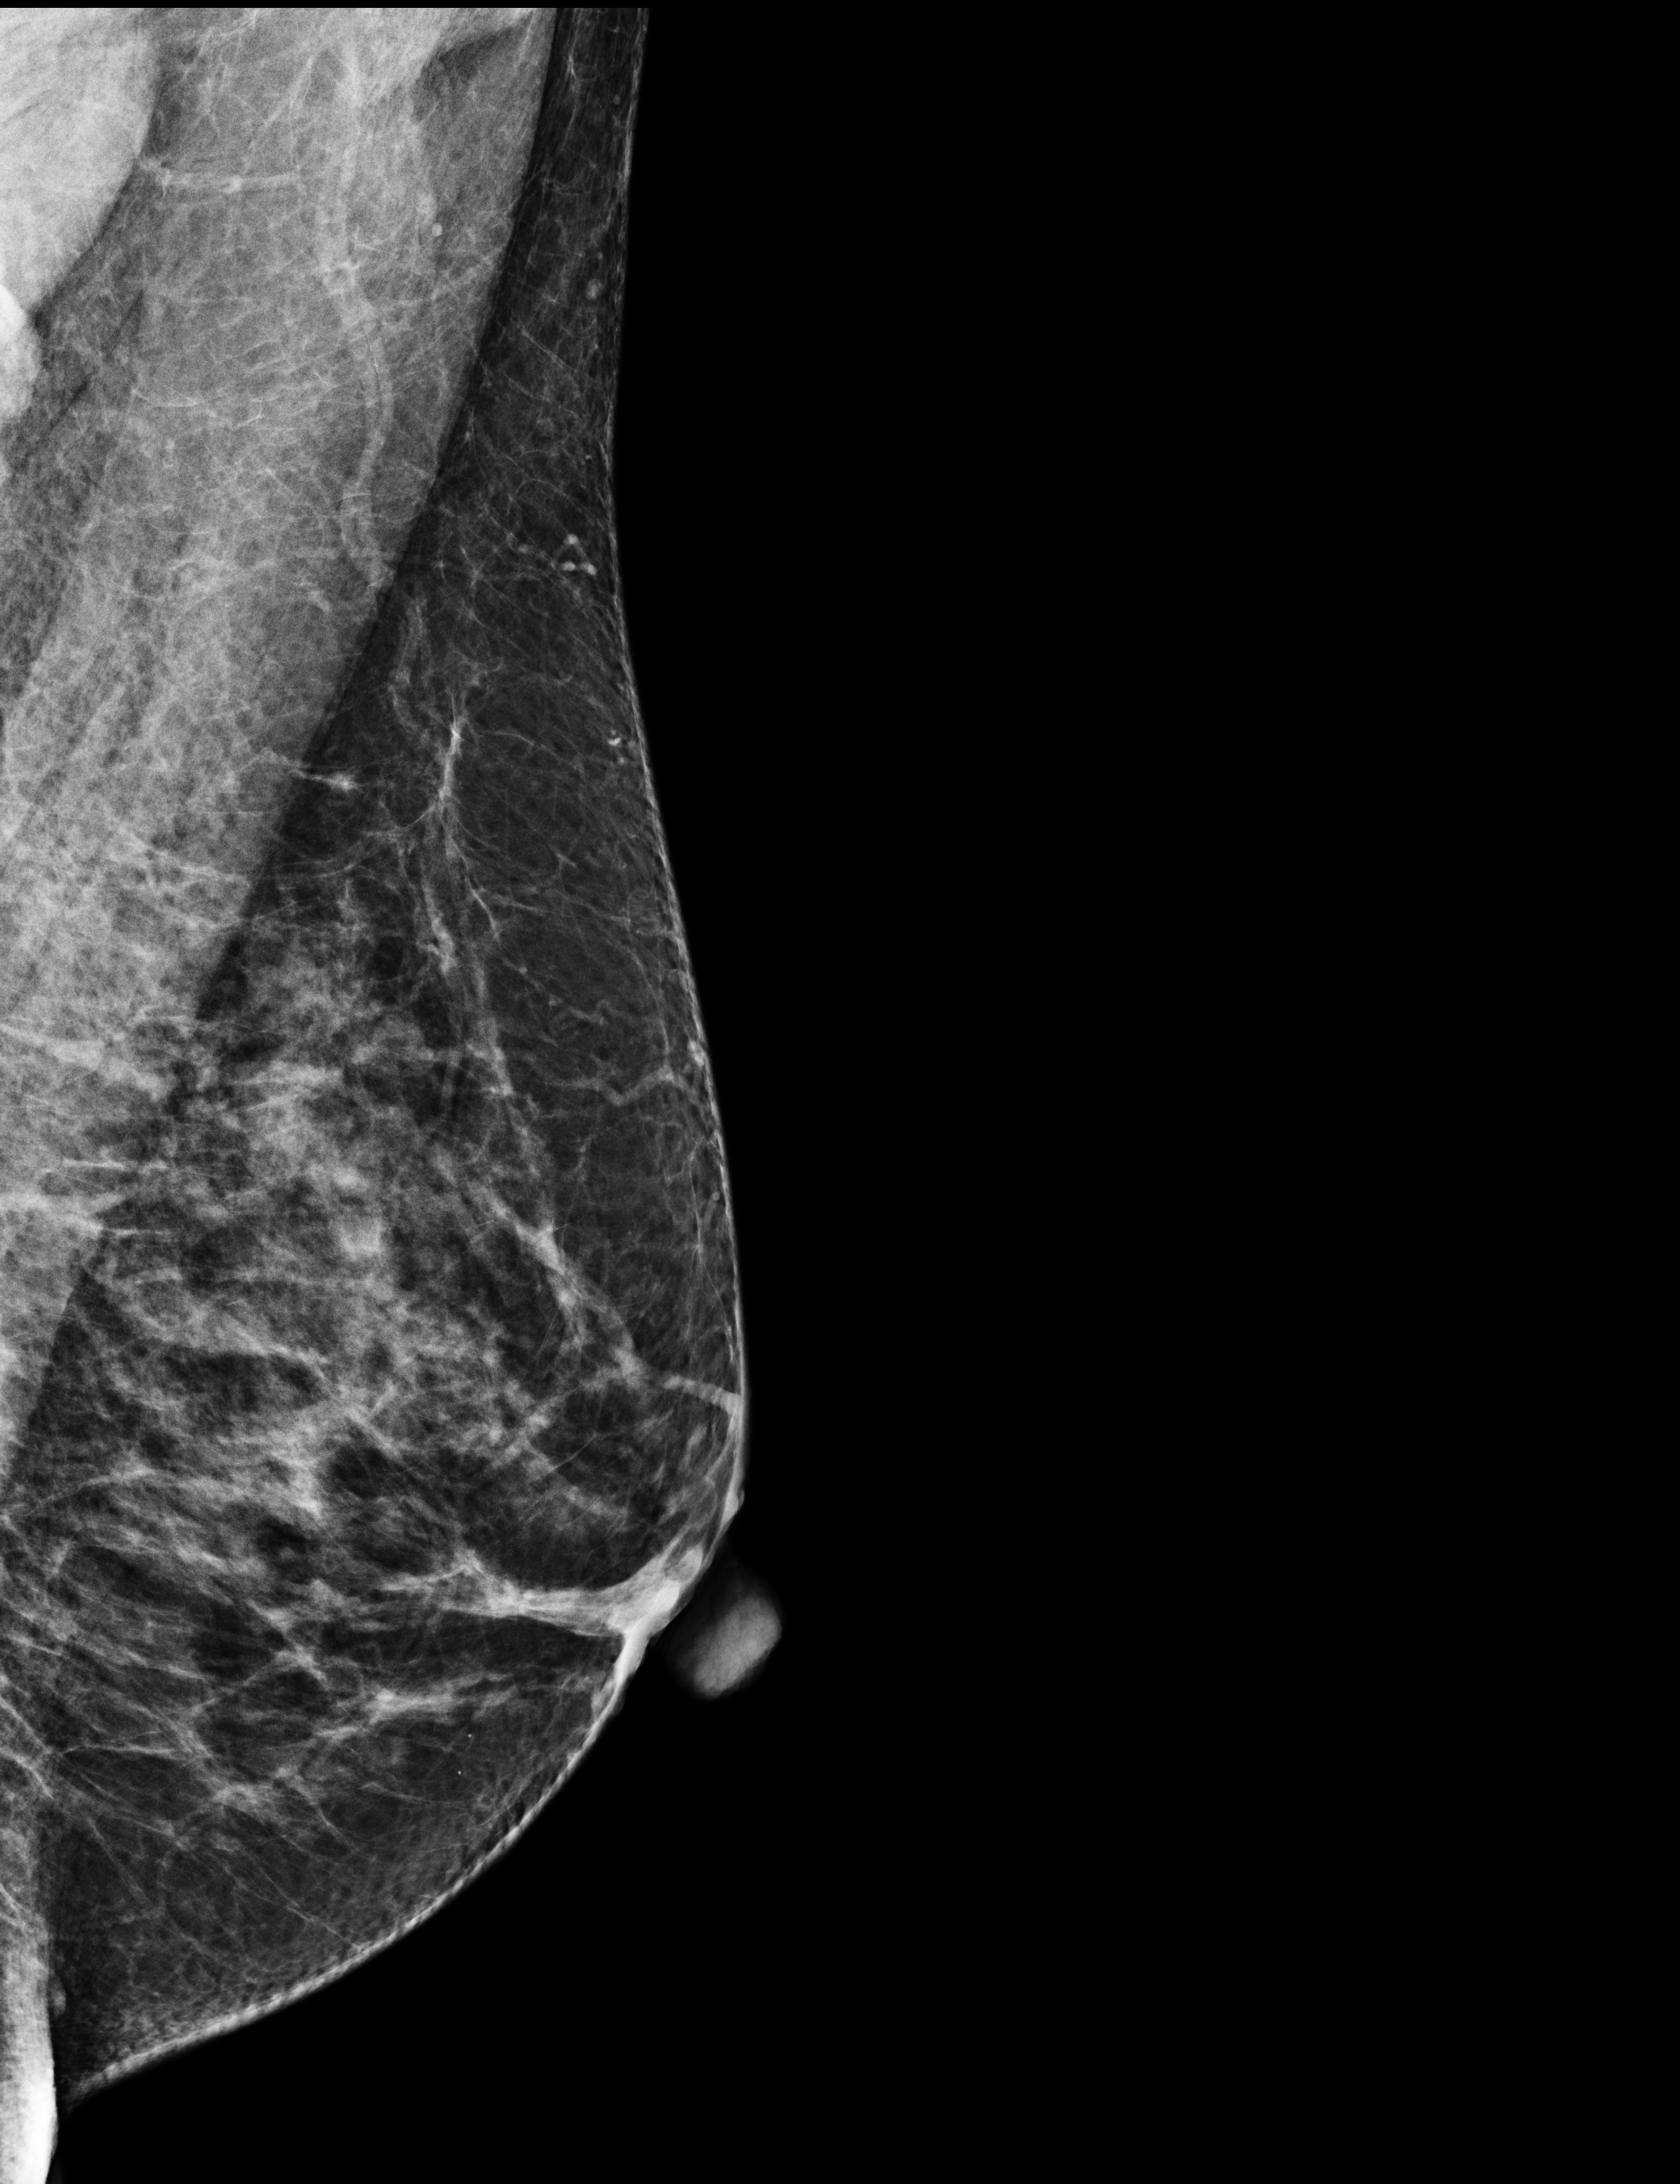
Screening examination; compressed breast thickness 61 mm; system: Selenia Dimensions. Female patient, age 62 years.
Image type: full-field digital mammogram. Breast: left. Projection: MLO view.